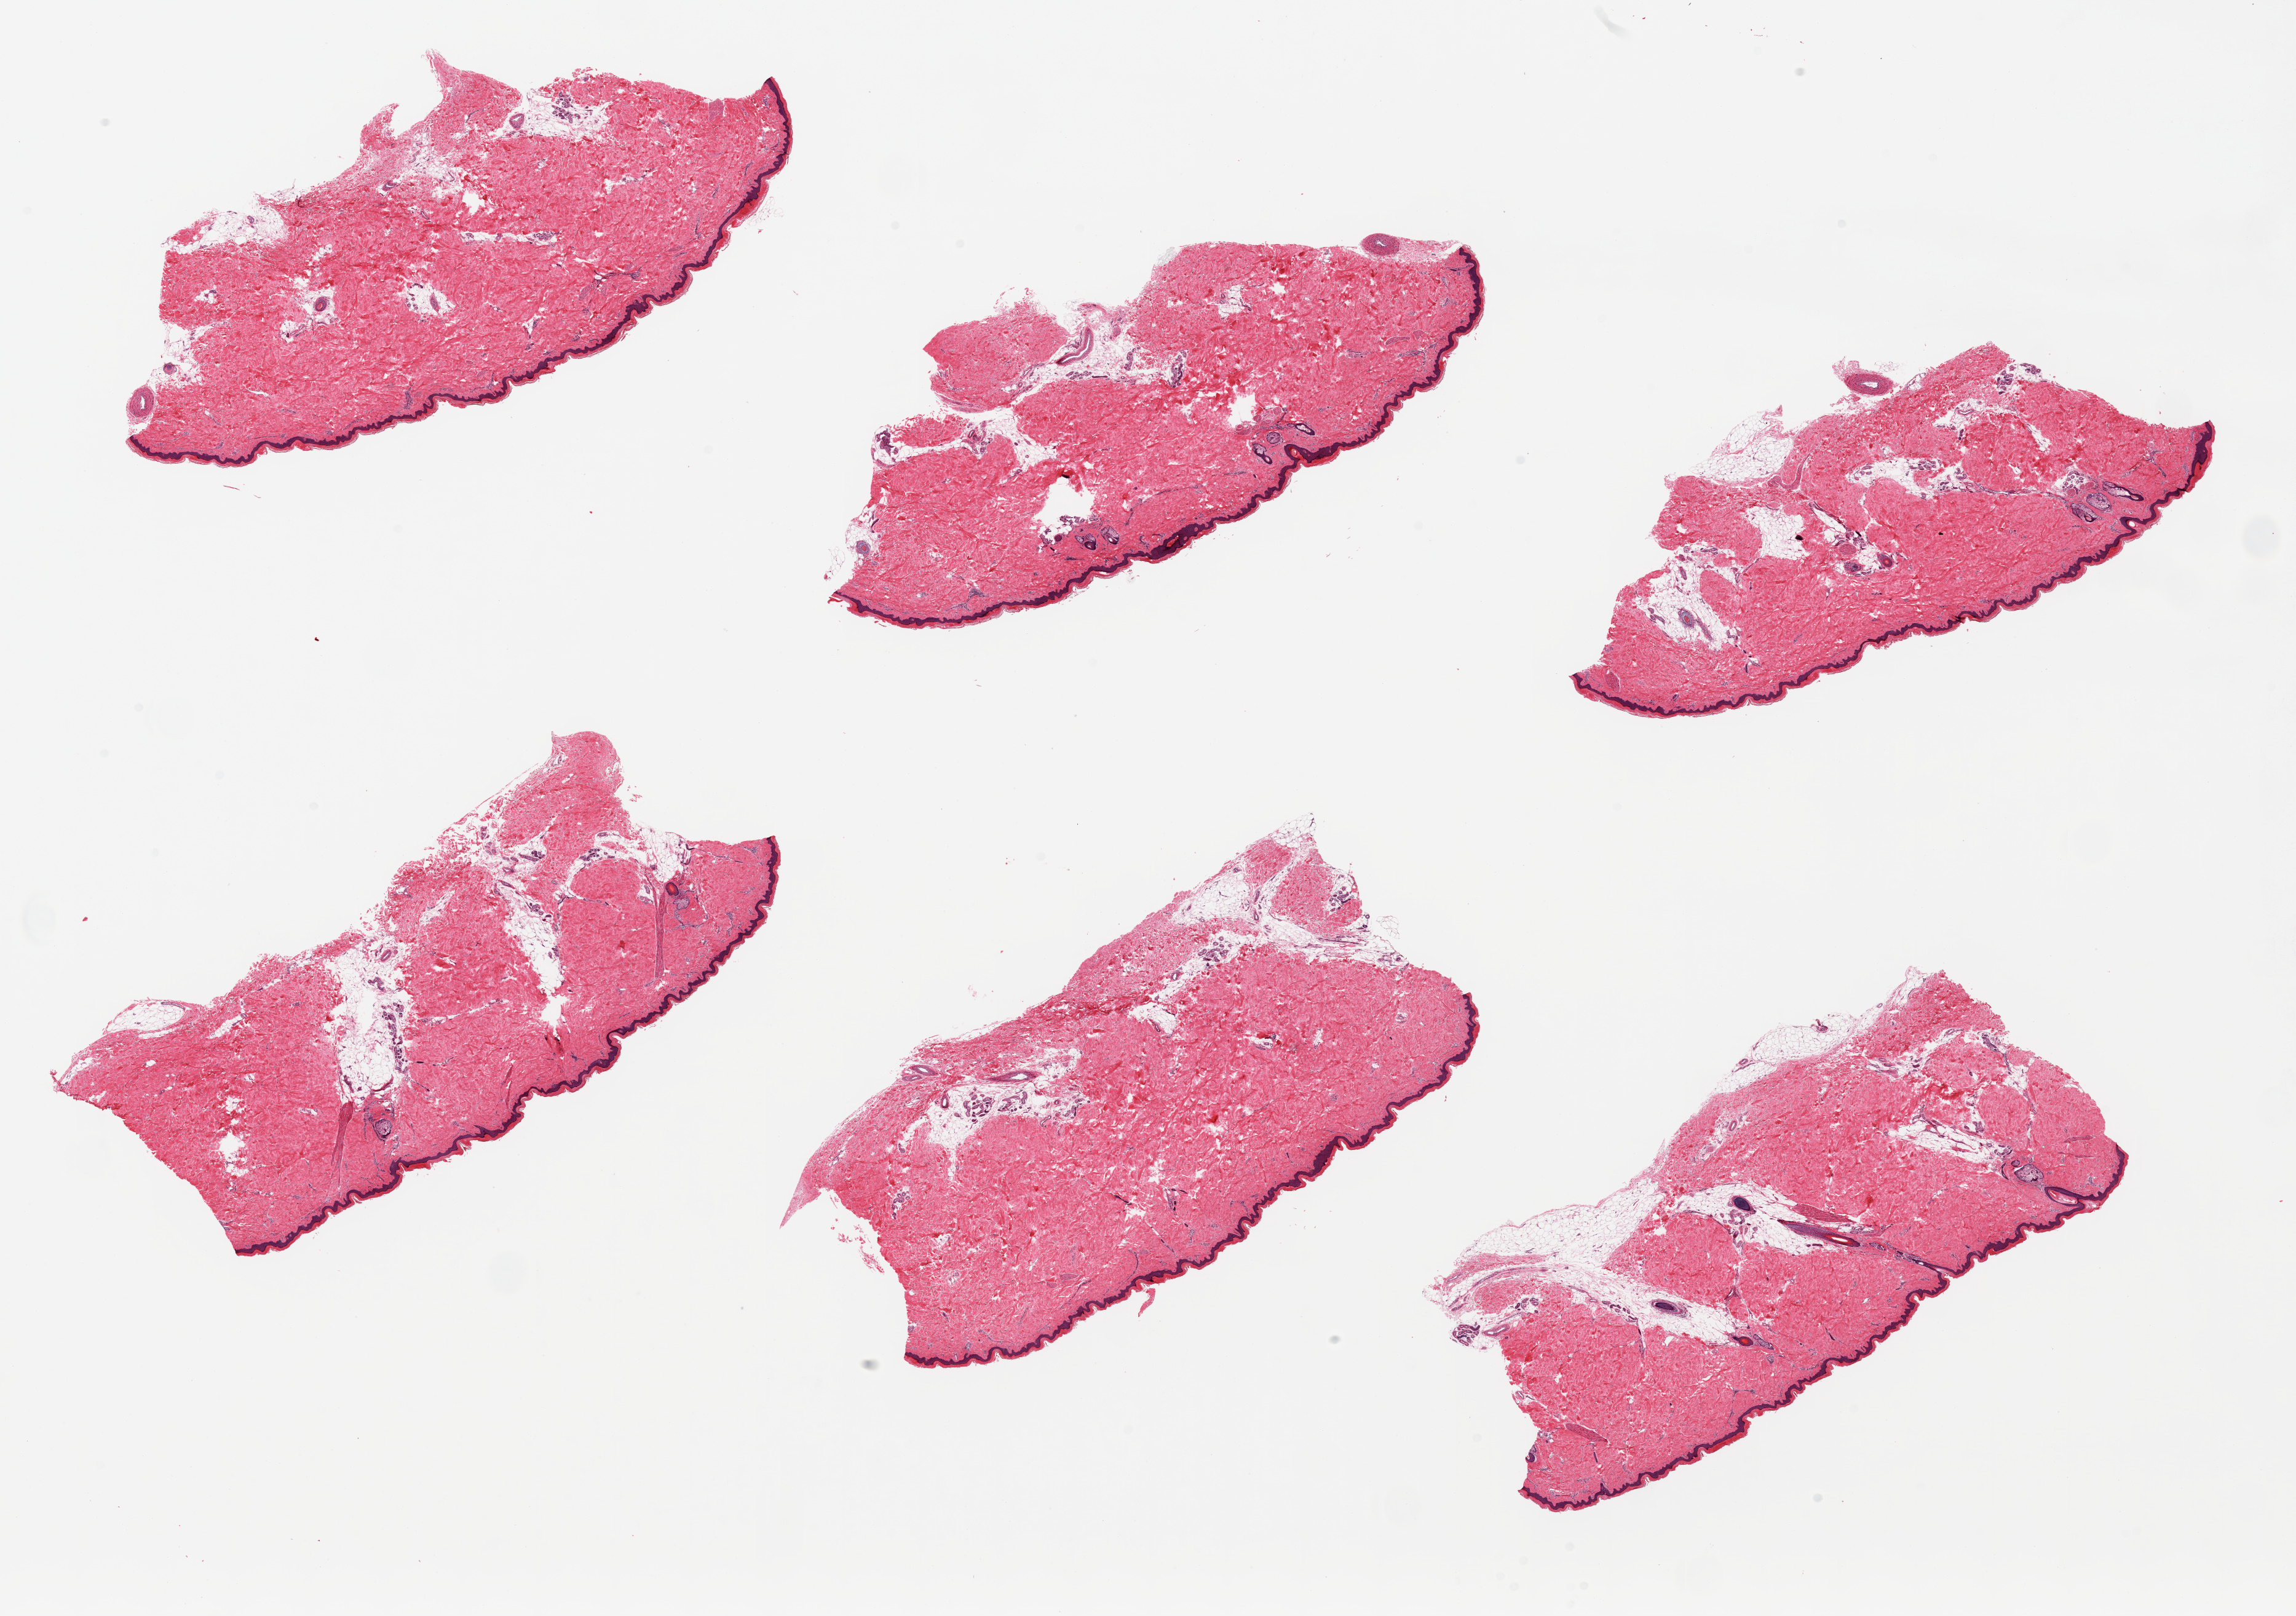
Whole-slide image, hematoxylin and eosin (H&E) stain, brightfield, whole scanned area (about 29.5 x 20.8 mm, slide scanned at 20x) shown as a low-resolution overview. PAXgene-fixed, paraffin-embedded tissue. Section of skin of lower leg (target tissue). Donor tissue sample. Donor sex: female.
- review note (as recorded): 6 pieces; 20% intradermal fat; well dissected